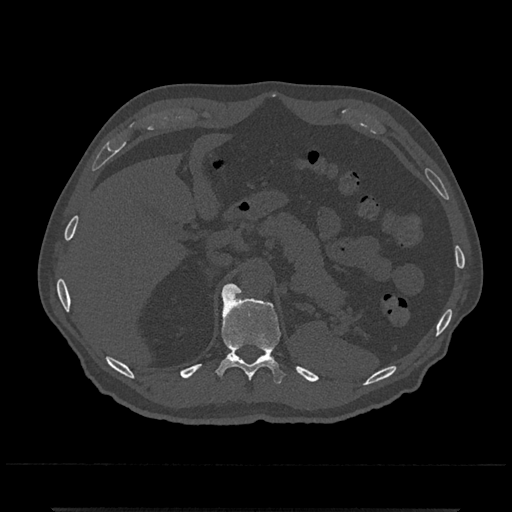
CT including the spine, one axial slice. Position 487 of 797 along the scan axis. Bone window (W 1800 / L 400 HU). 0.5 mm slice thickness. 512 × 512 image matrix, field of view 393 × 393 mm. Male patient, age 67 years. From the clinical record (not read from this slice): primary cancer: prostate.
Outlined on this slice (semi-automatic segmentation, software-assisted and operator-edited):
- T11 vertebra: box from (x=217, y=285) to (x=285, y=384) px
- T12 vertebra: (x=223, y=284)–(x=241, y=295)